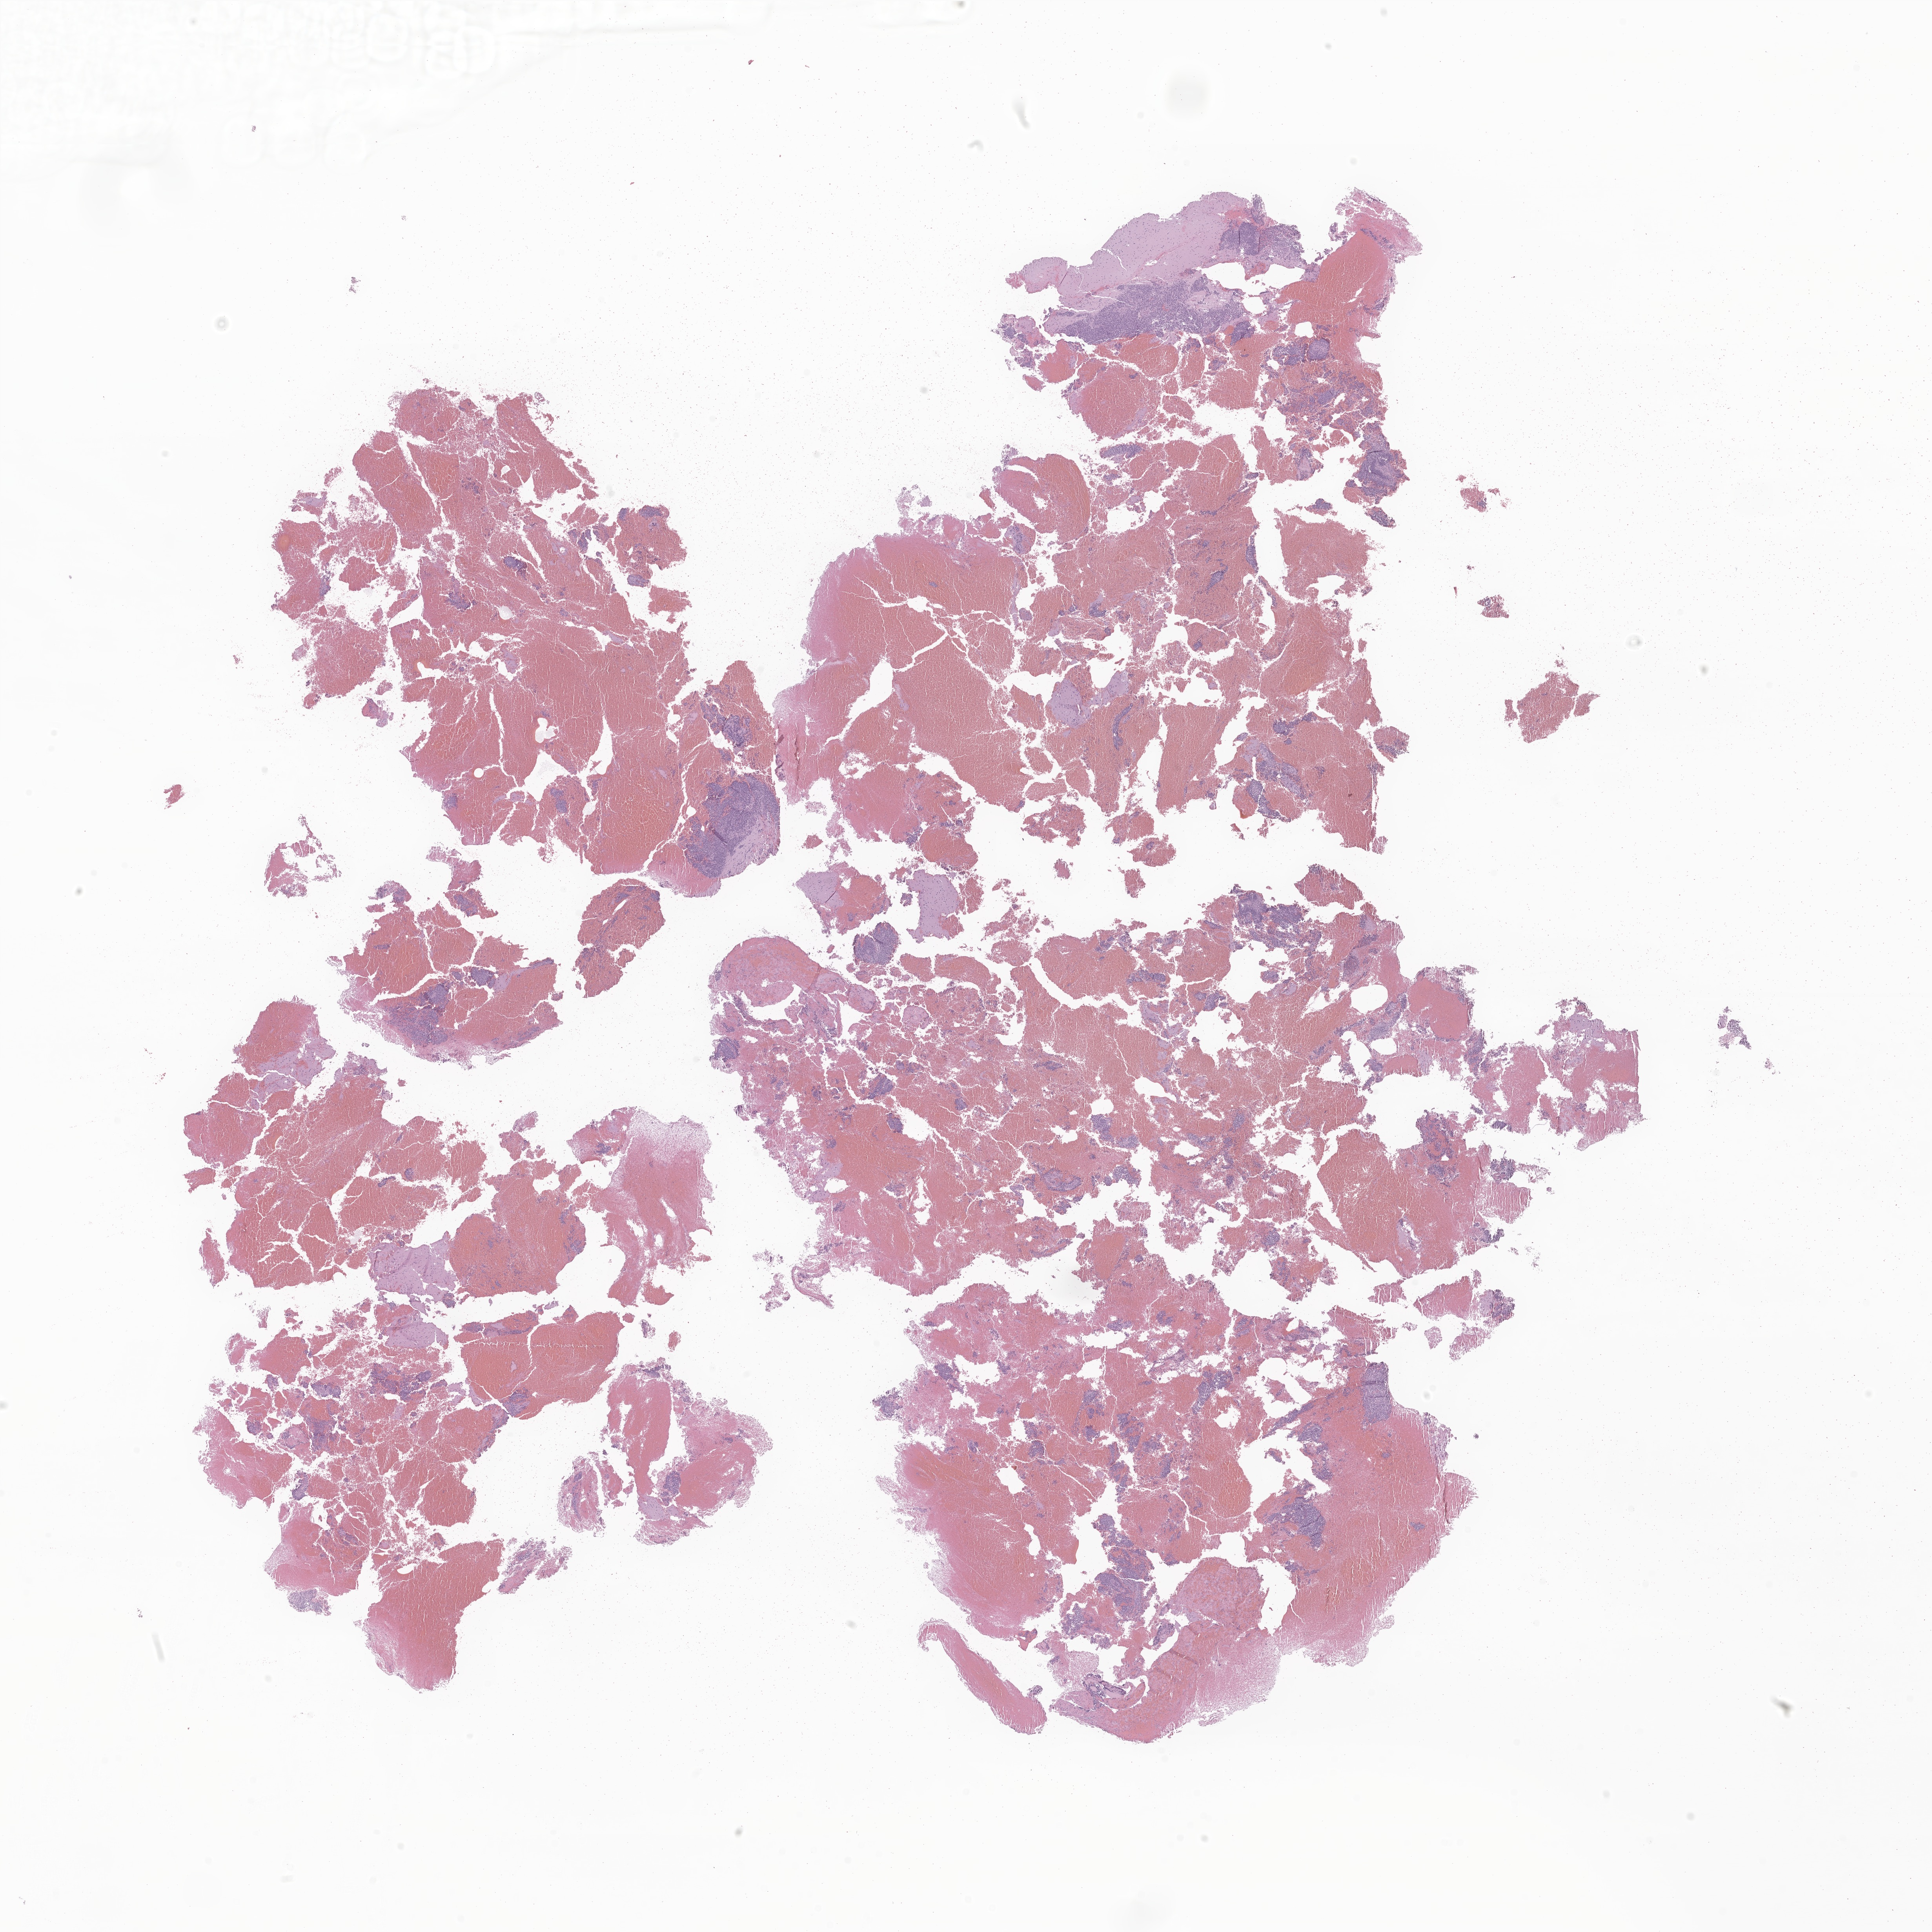
Whole-slide image, H&E stain of tumor tissue from the frontal lobe, a low-resolution overview of the entire scanned area, about 20.8 x 20.8 mm; formalin-fixed paraffin-embedded section. Male patient, age 167 months (13 years 11 months).
Recorded diagnosis: Glioma, malignant.